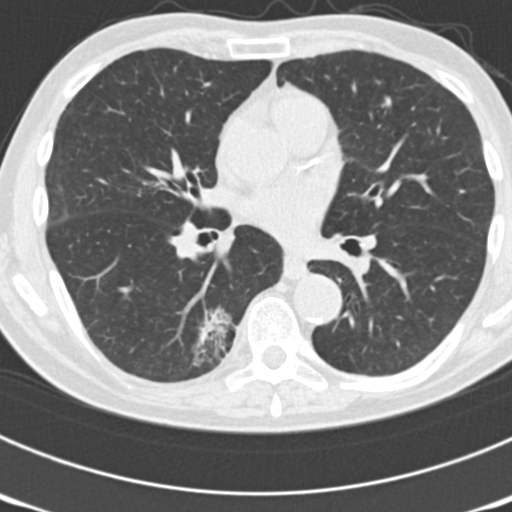
Low-dose screening chest CT, axial slice, third annual screen, lung window (W 1500 / L -600 HU), 120 kVp, slice 82 of 177 in the series, 512 × 512 image matrix, field of view 300 × 300 mm. Male, age 70 years at enrolment. Current smoker at enrolment.
Expert-annotated lung lesion, bounding box <148,302,239,384> (left, top, right, bottom; pixels). The screening reader recorded 3 non-calcified nodules or masses ≥4 mm on this exam (right upper lobe, left upper lobe, right lower lobe); which of them this box marks is not recorded. Official screen result: positive, other. Later outcome: lung cancer diagnosed 14 days after this screen — bronchiolo-alveolar adenocarcinoma, NOS, right lower lobe, poorly differentiated (G3), stage IB (AJCC 6th edition), 30 mm at pathology.